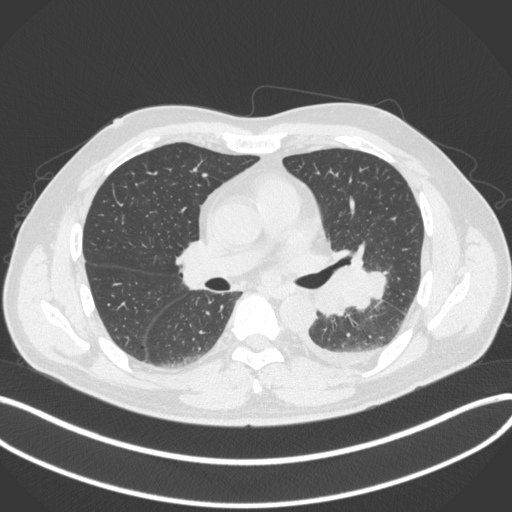
Chest CT, one axial slice. Slice 200 of 350 in the series (ordered by position). Lung window (W 1500 / L -600 HU). 512 × 512 image matrix, field of view 400 × 400 mm. Male patient, age 58 years. From the clinical record (not read from this slice): clinical TNM (as recorded): T3 N1 M1b; histopathological grade: G3.
Outlined on this slice (bounding box drawn by a radiologist):
- lung tumour (recorded histology: small cell carcinoma): bounding box [x1, y1, x2, y2] px = [308, 263, 387, 325]